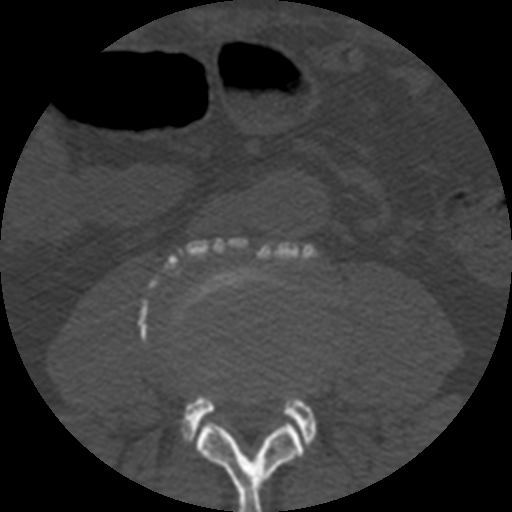
CT including the spine, one axial slice. Slice 107 of 508 in the series (ordered by position). Reconstruction kernel STANDARD. 120 kVp. Bone window (W 1800 / L 400 HU). 1.25 mm slice thickness. 512 × 512 image matrix, field of view 160 × 160 mm. Patient age 57 years. From the clinical record (not read from this slice): primary cancer: prostate.
Annotated regions visible in this slice (semi-automatic segmentation, software-assisted and operator-edited):
- L3 vertebra: box from (x=196, y=399) to (x=303, y=512) px
- L4 vertebra: (x=139, y=238)–(x=319, y=448)